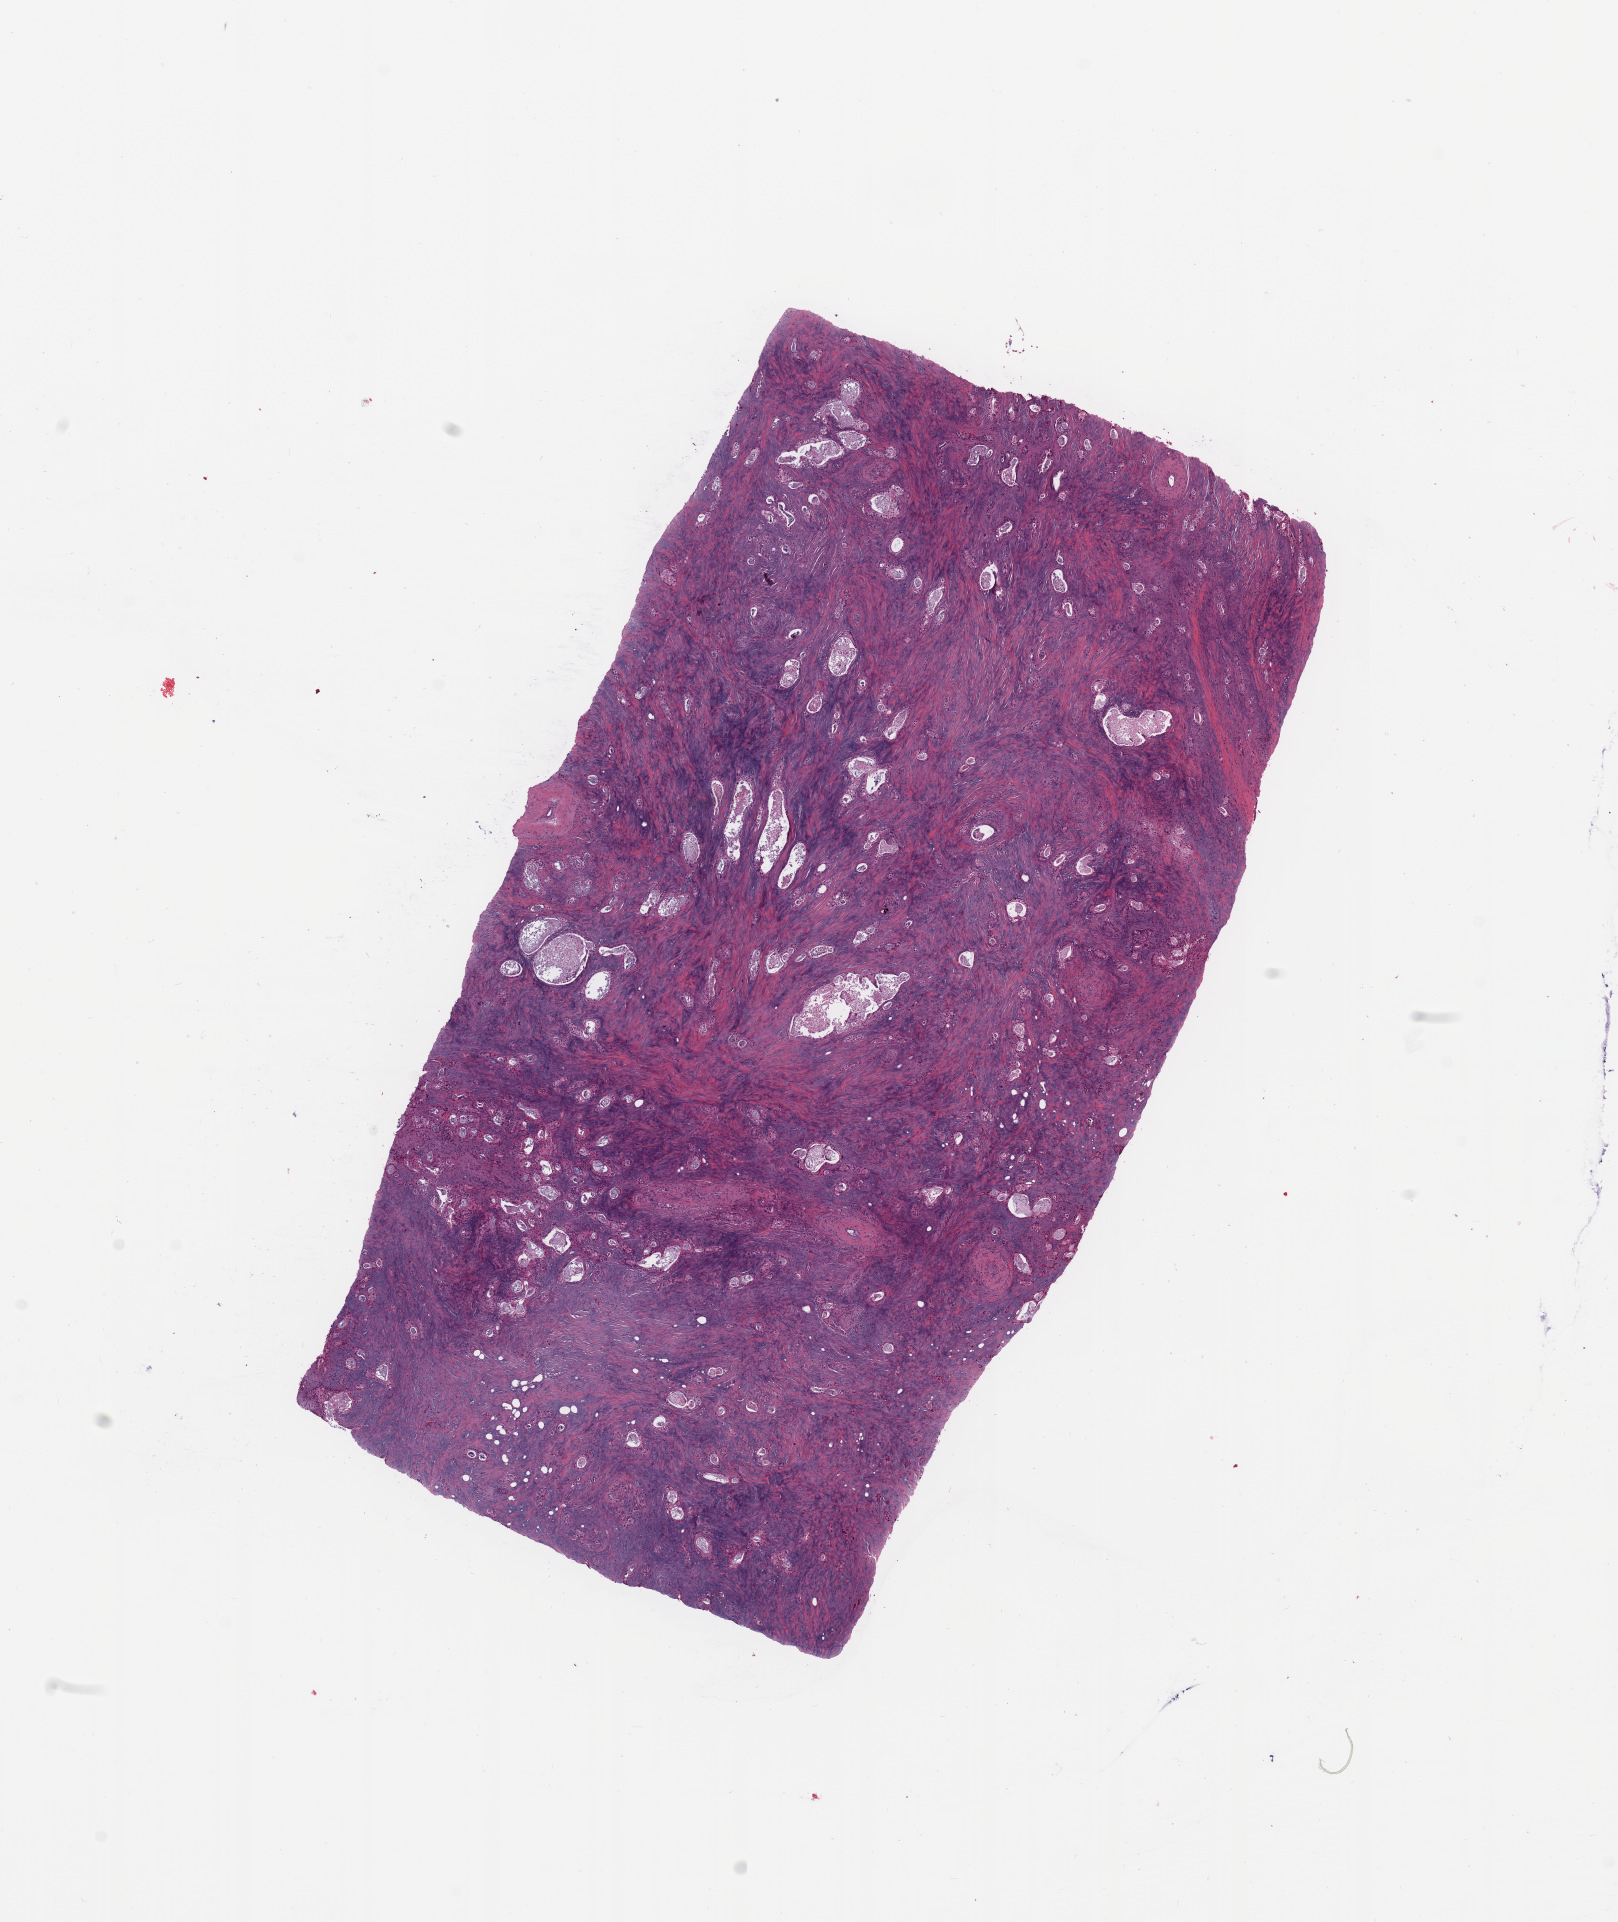
Digitized Hematoxylin and eosin (H&E) stained tissue section (whole slide) — shown as a low-resolution overview of the whole scanned area (about 12.8 x 15.2 mm, from a 20x scan). Tumour tissue sample, sampled site: pancreas. Male, 84 y/o.
Histologic diagnosis: Infiltrating duct carcinoma, NOS.